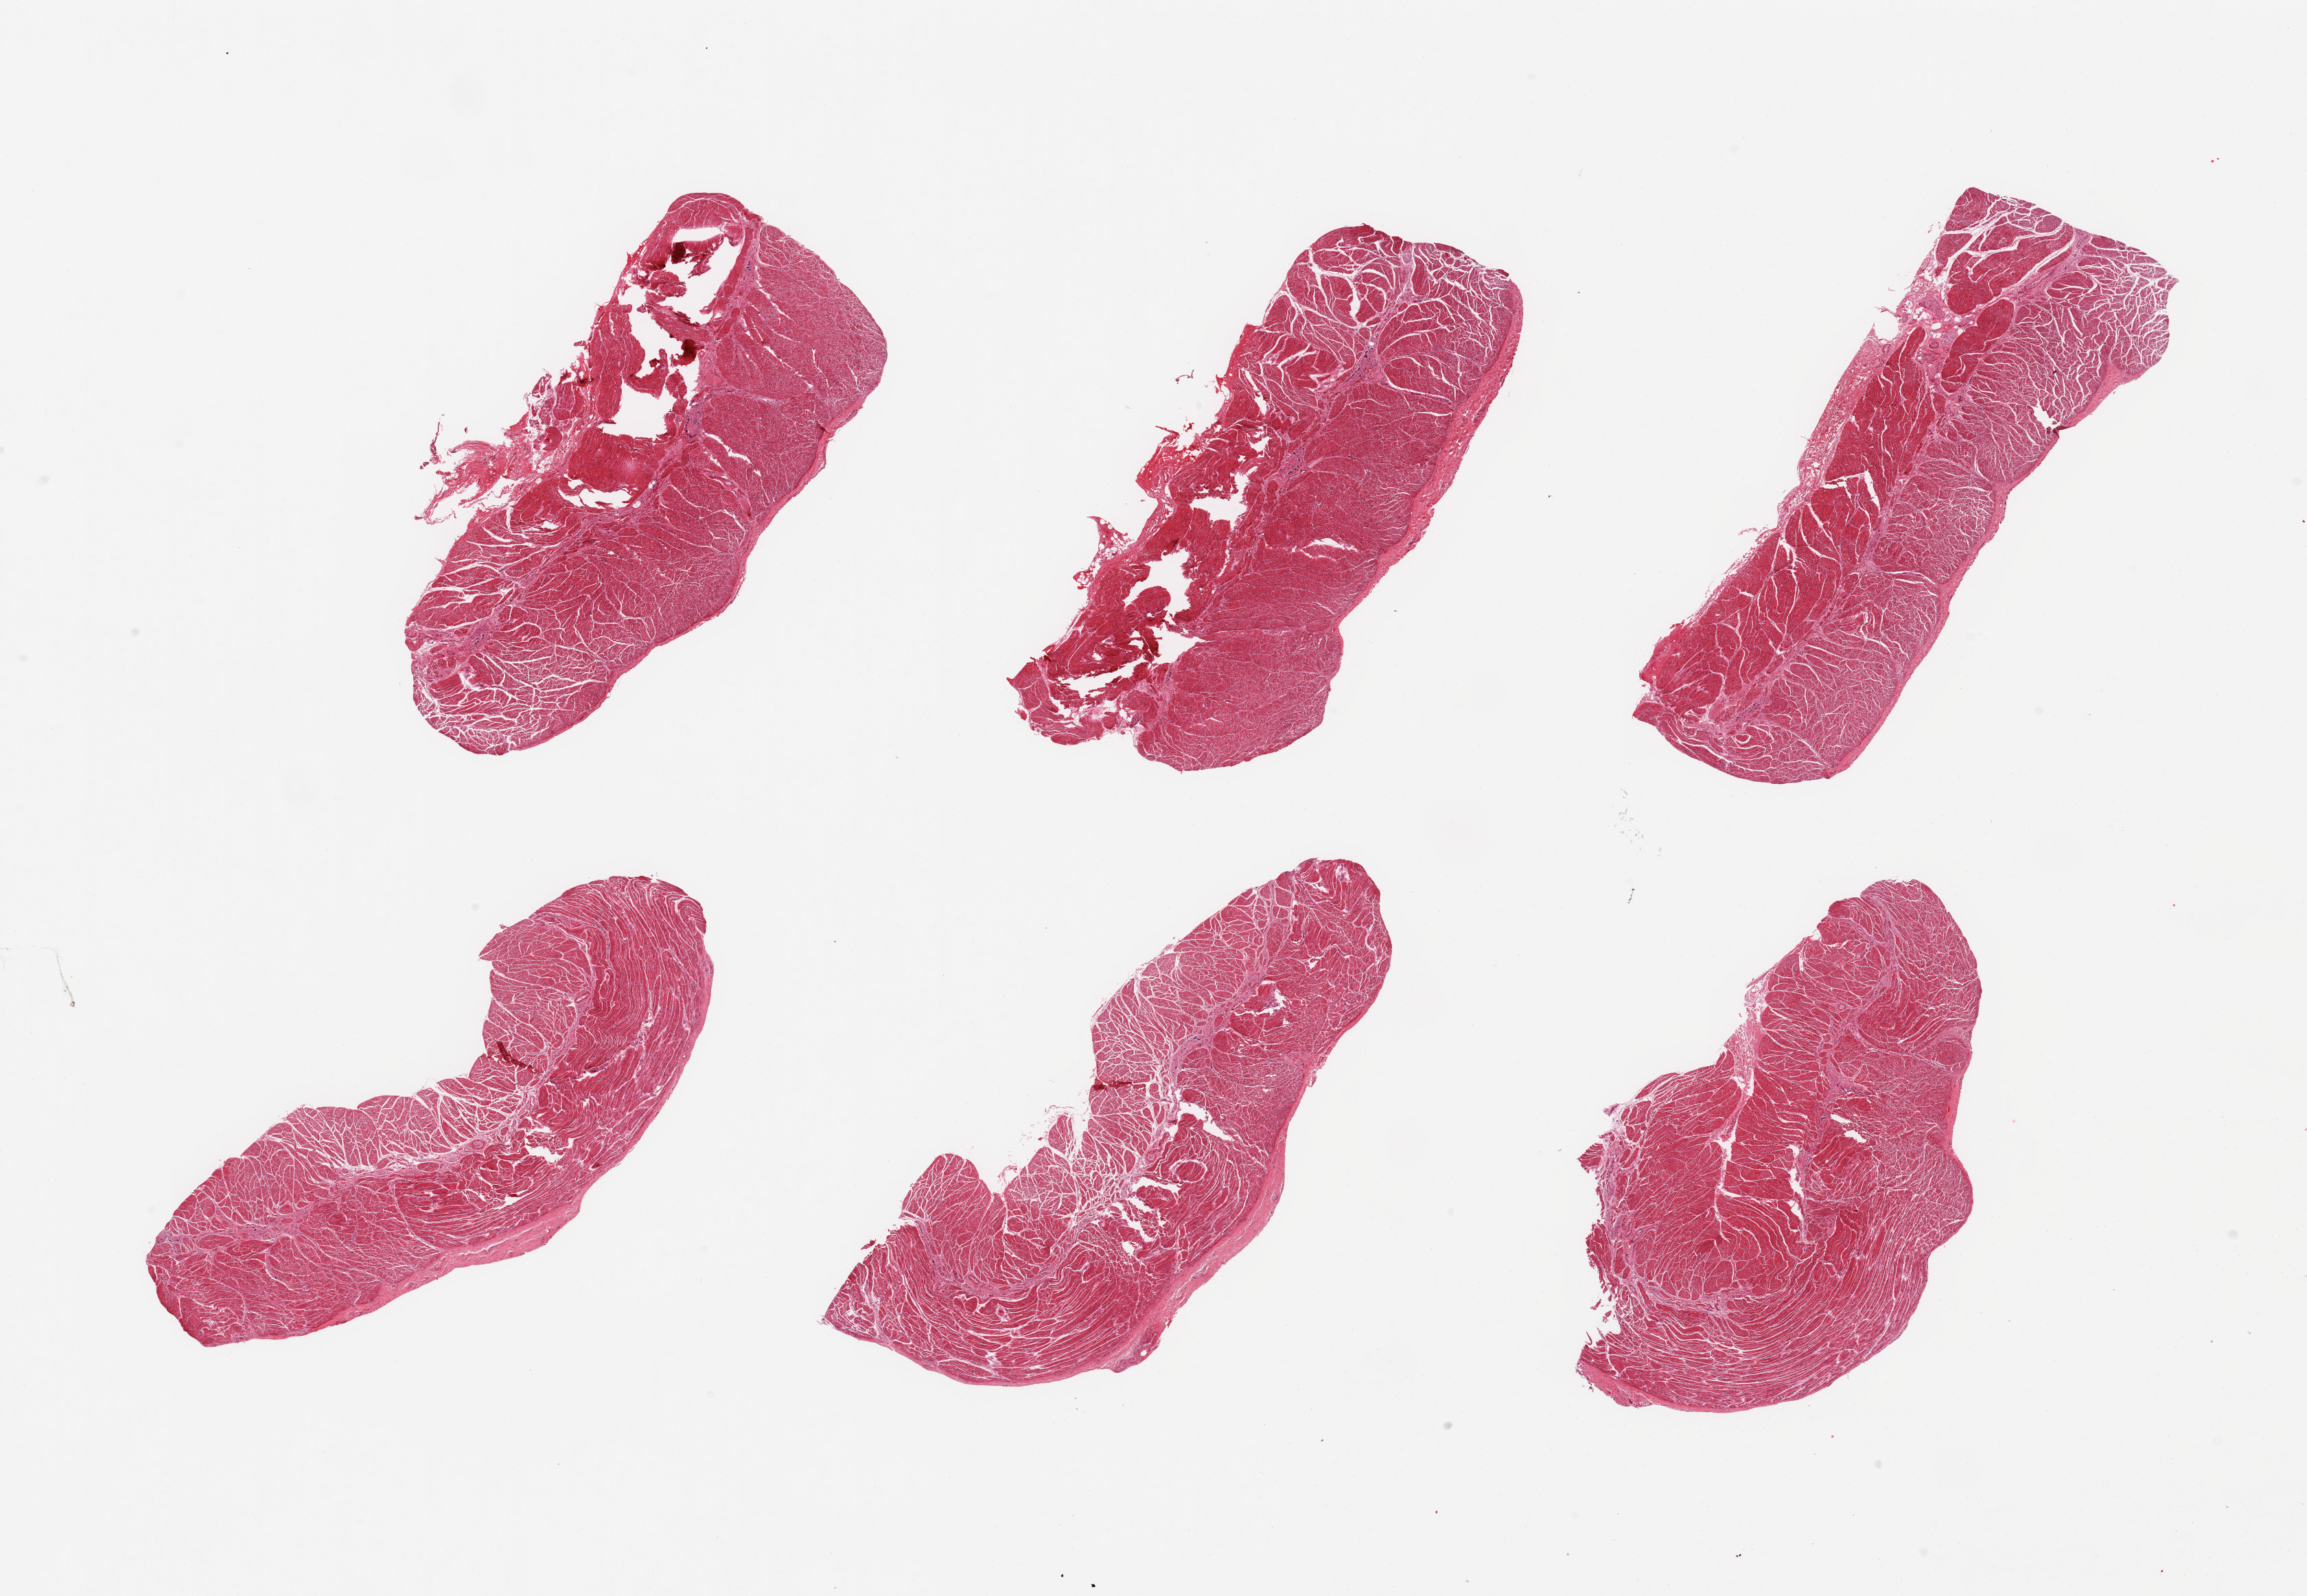
Digitized haematoxylin and eosin-stained section — low-resolution overview of the scanned area, about 26.6 x 18.4 mm, PAXgene-fixed paraffin-embedded (PFPE) section, section of gastroesophageal junction (target tissue), tissue donor sample. Donor sex: male.
* pathologist's review note for this sample: 6 pieces, confirmed target muscularis